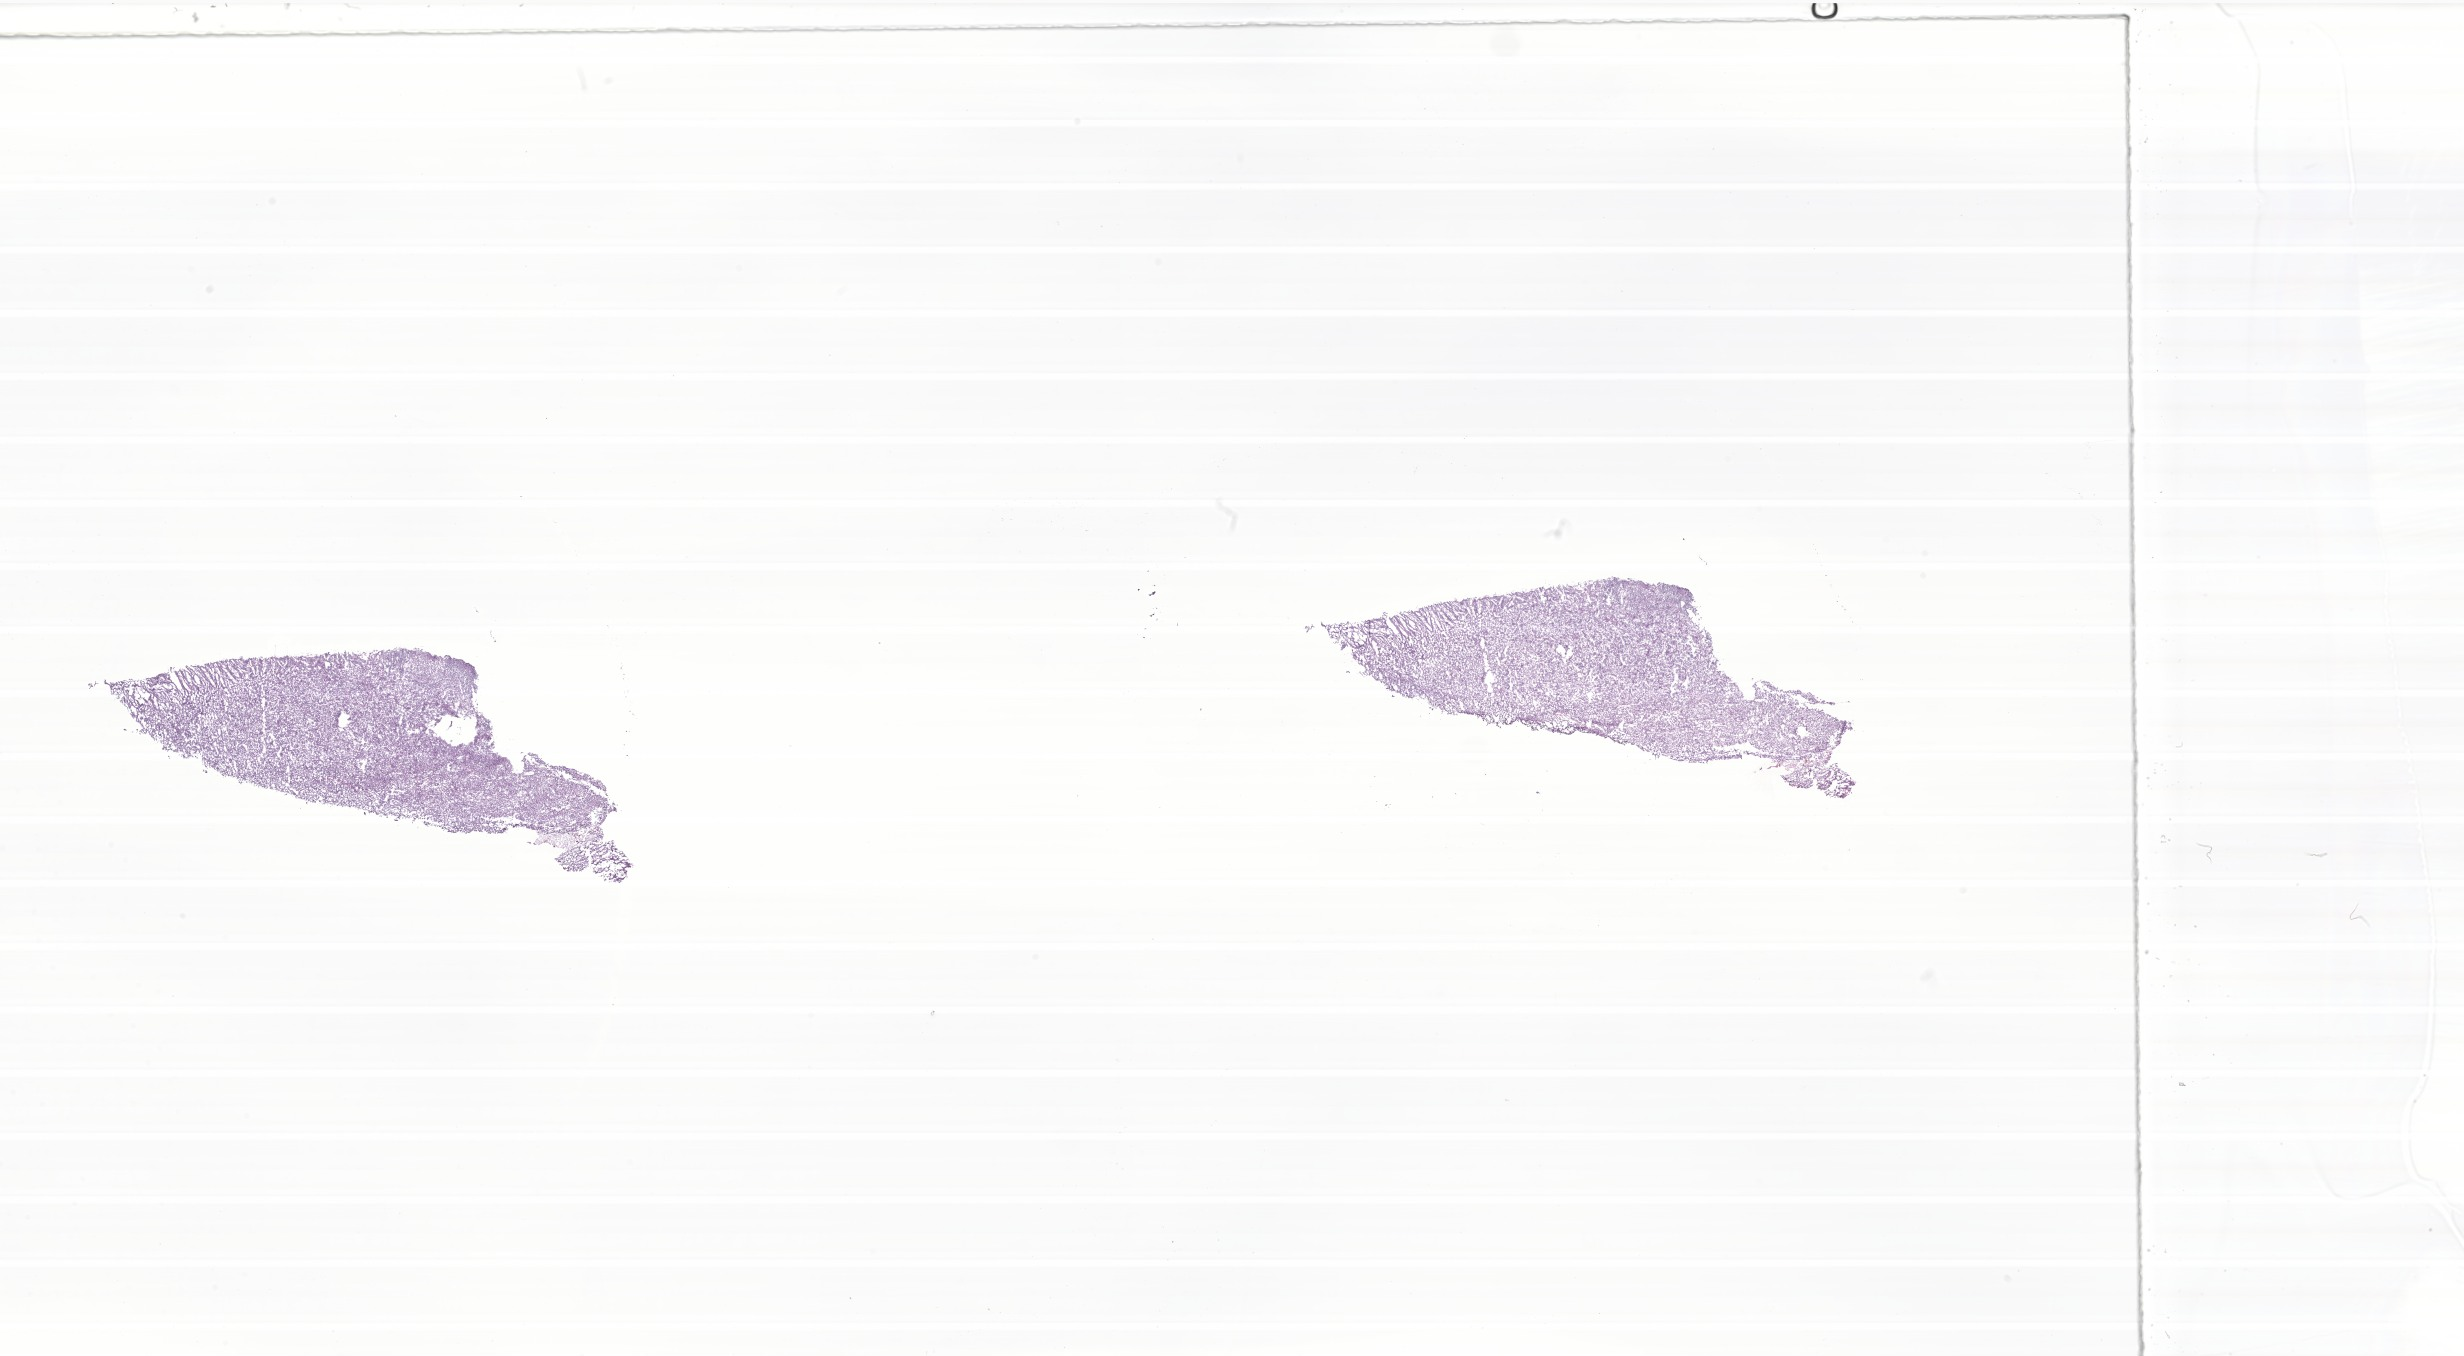
Digitized haematoxylin and eosin-stained section of tumor tissue from the brain — low-resolution overview of the scanned area, about 41.6 x 22.9 mm. Cryosection (OCT / tissue freezing medium). Female patient, age 73 months.
Diagnosis: Medulloblastoma, NOS.